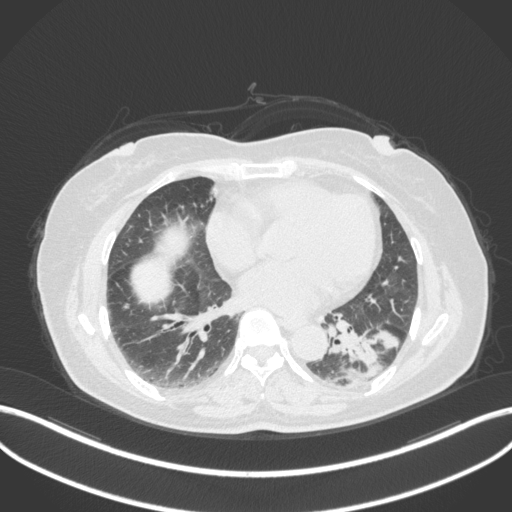
Chest CT, one axial slice; slice 156 of 307 in the series (ordered by position); reconstruction kernel B31f; 120 kVp; lung window (W 1500 / L -600 HU); 1 mm slice thickness; 512 × 512 image matrix, field of view 400 × 400 mm. Female patient, age 59 years. Case-level facts recorded for this patient, not image findings: clinical TNM (as recorded): T2a N0 M0; histopathological grade: G2-3.
Outlined on this slice (bounding box drawn by a radiologist):
- lung tumour (recorded histology: adenocarcinoma): bounding box <326,322,399,387> (left, top, right, bottom; pixels)